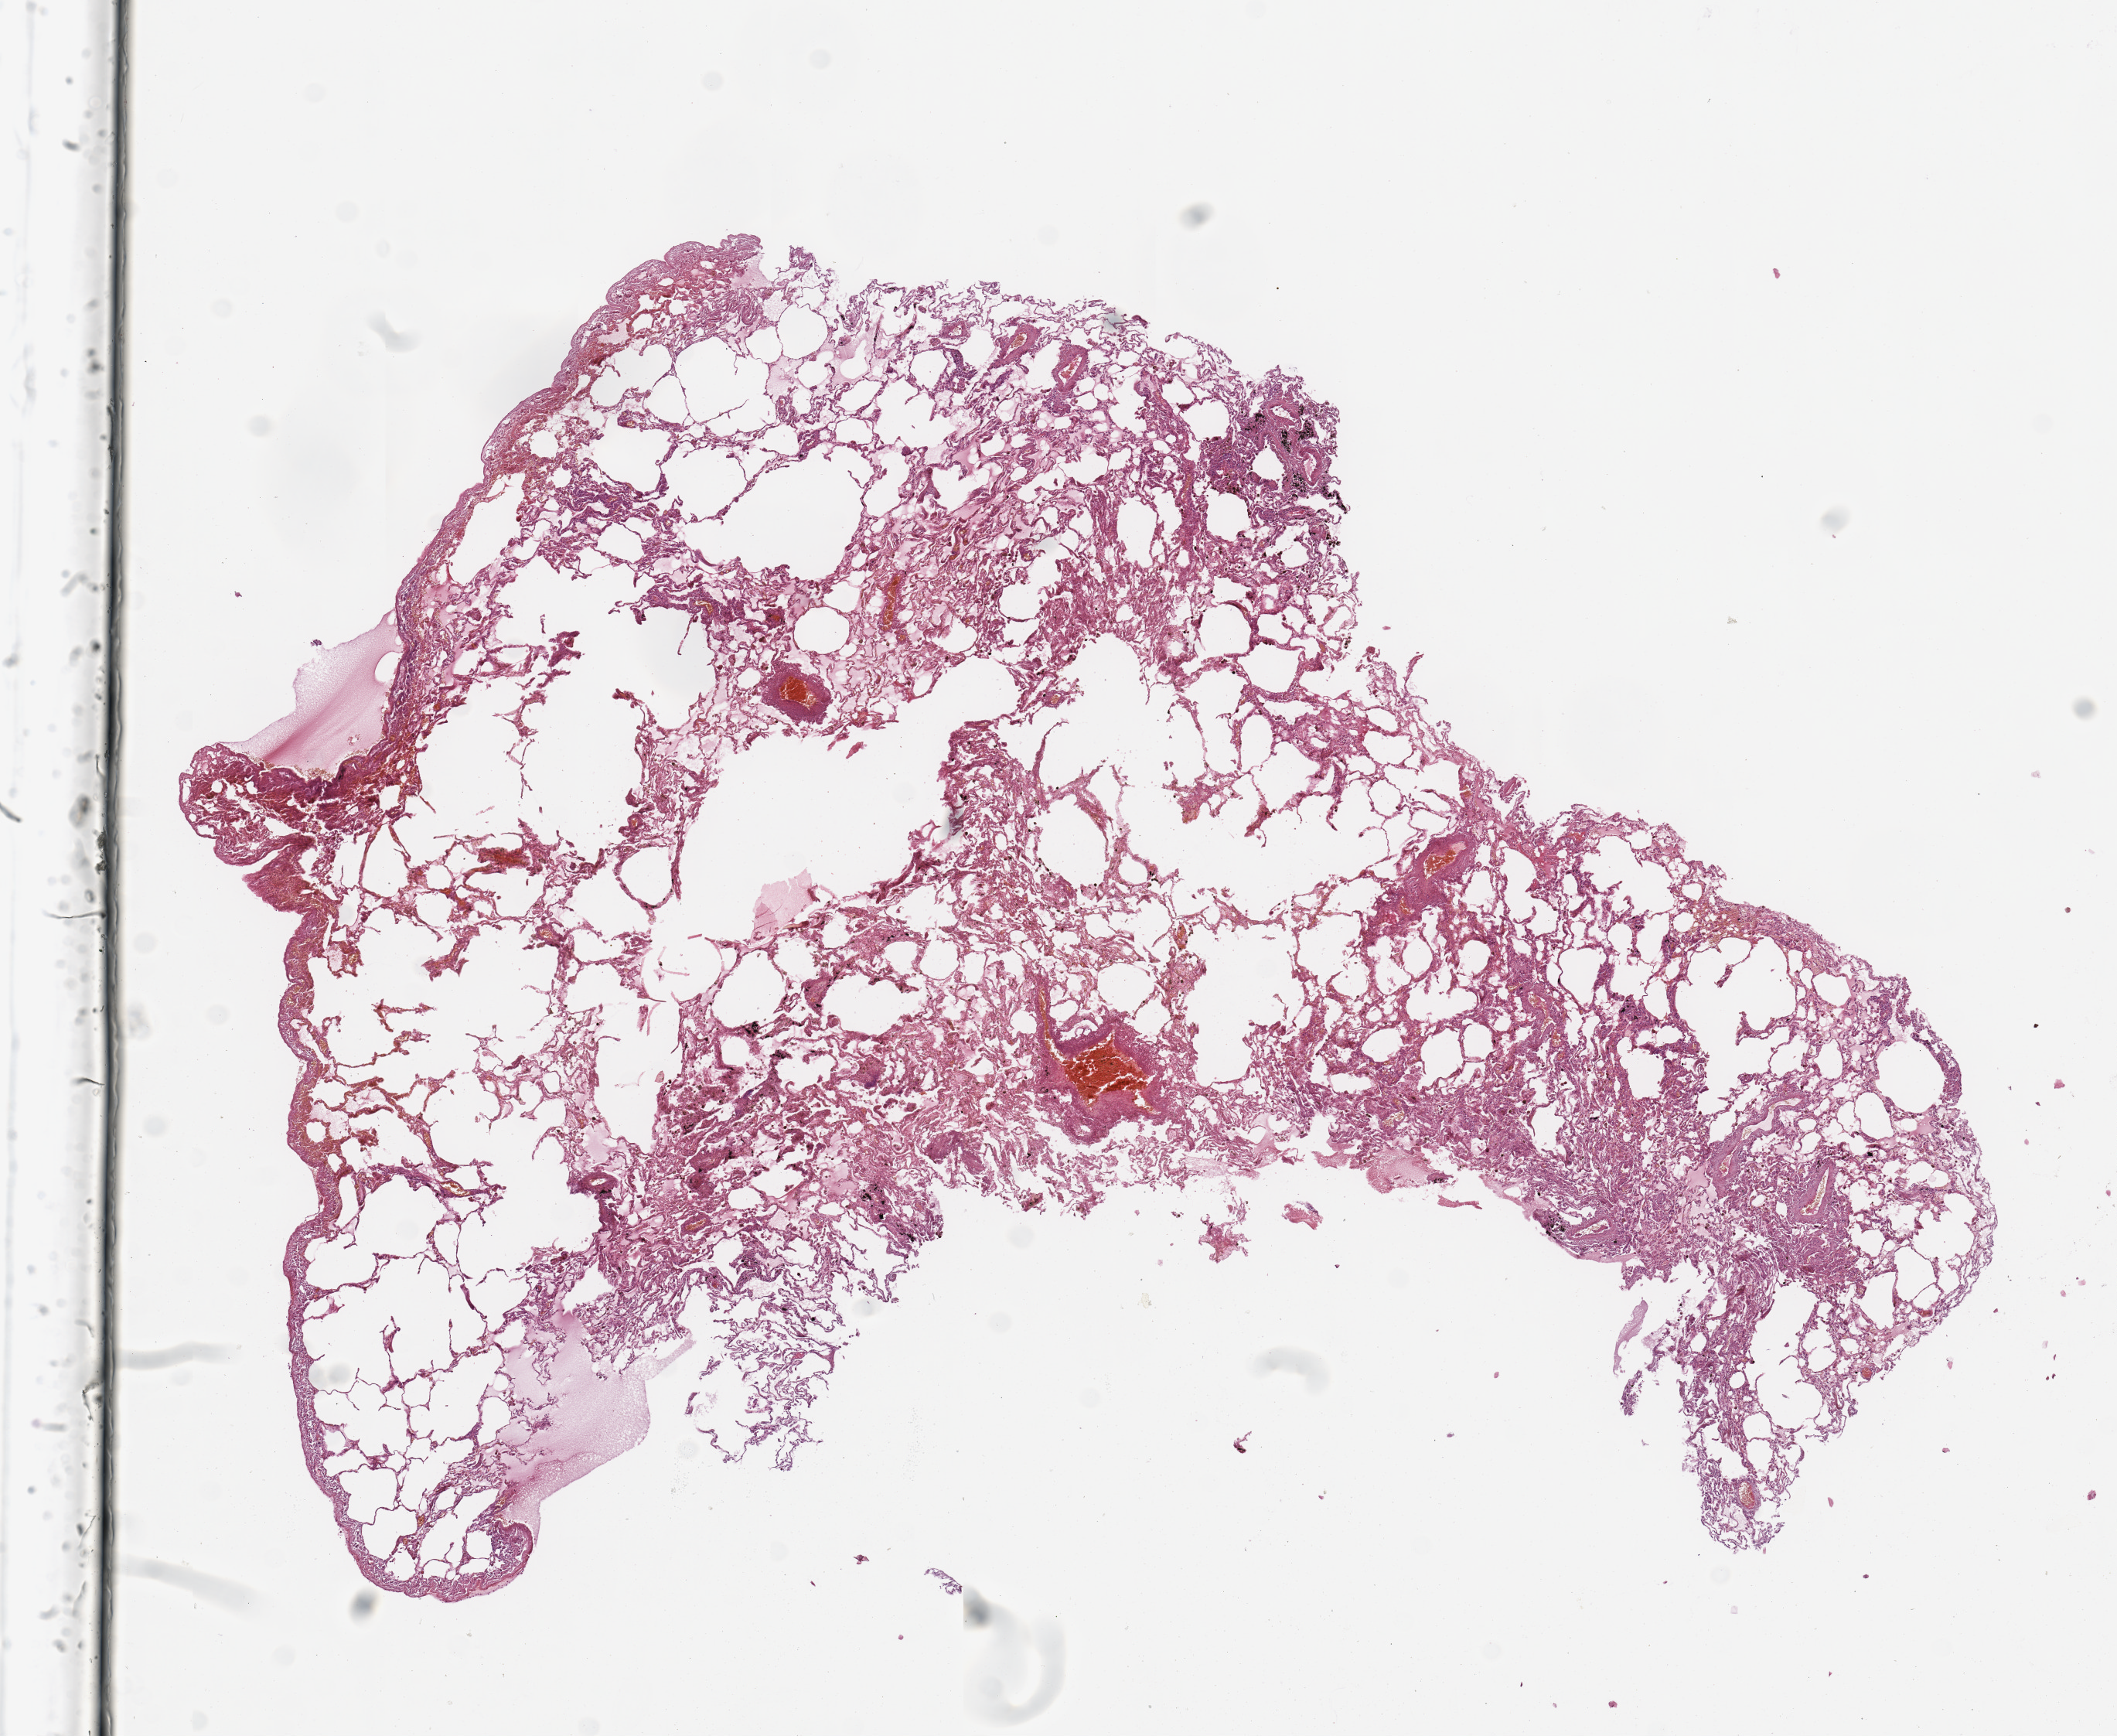
Whole-slide histology image, H&E-stained — a low-resolution overview of the entire scanned area, about 10.8 x 8.9 mm, normal (non-tumour) tissue sample, sampled site: lung. 65-year-old male patient.
This section: normal (non-tumour) tissue from the same patient. Patient diagnosis: Squamous cell carcinoma, NOS.